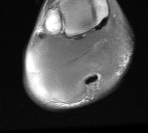
MRI of an extremity soft-tissue mass, one axial slice. Slice 13 of 76 in the series (ordered by position). MR volume resampled by the dataset authors to the PET/CT grid (not the native acquisition matrix). 148 × 133 image matrix, field of view 145 × 130 mm. Male patient. From the clinical record (not read from this slice): histological type: liposarcoma - round cell; grade: high; site of the primary tumour: right calf.
Structures marked on this image (expert contour drawn on MRI and transferred to this co-registered scan by the dataset authors):
- gross tumour volume (mass): box from (x=27, y=21) to (x=128, y=104) px